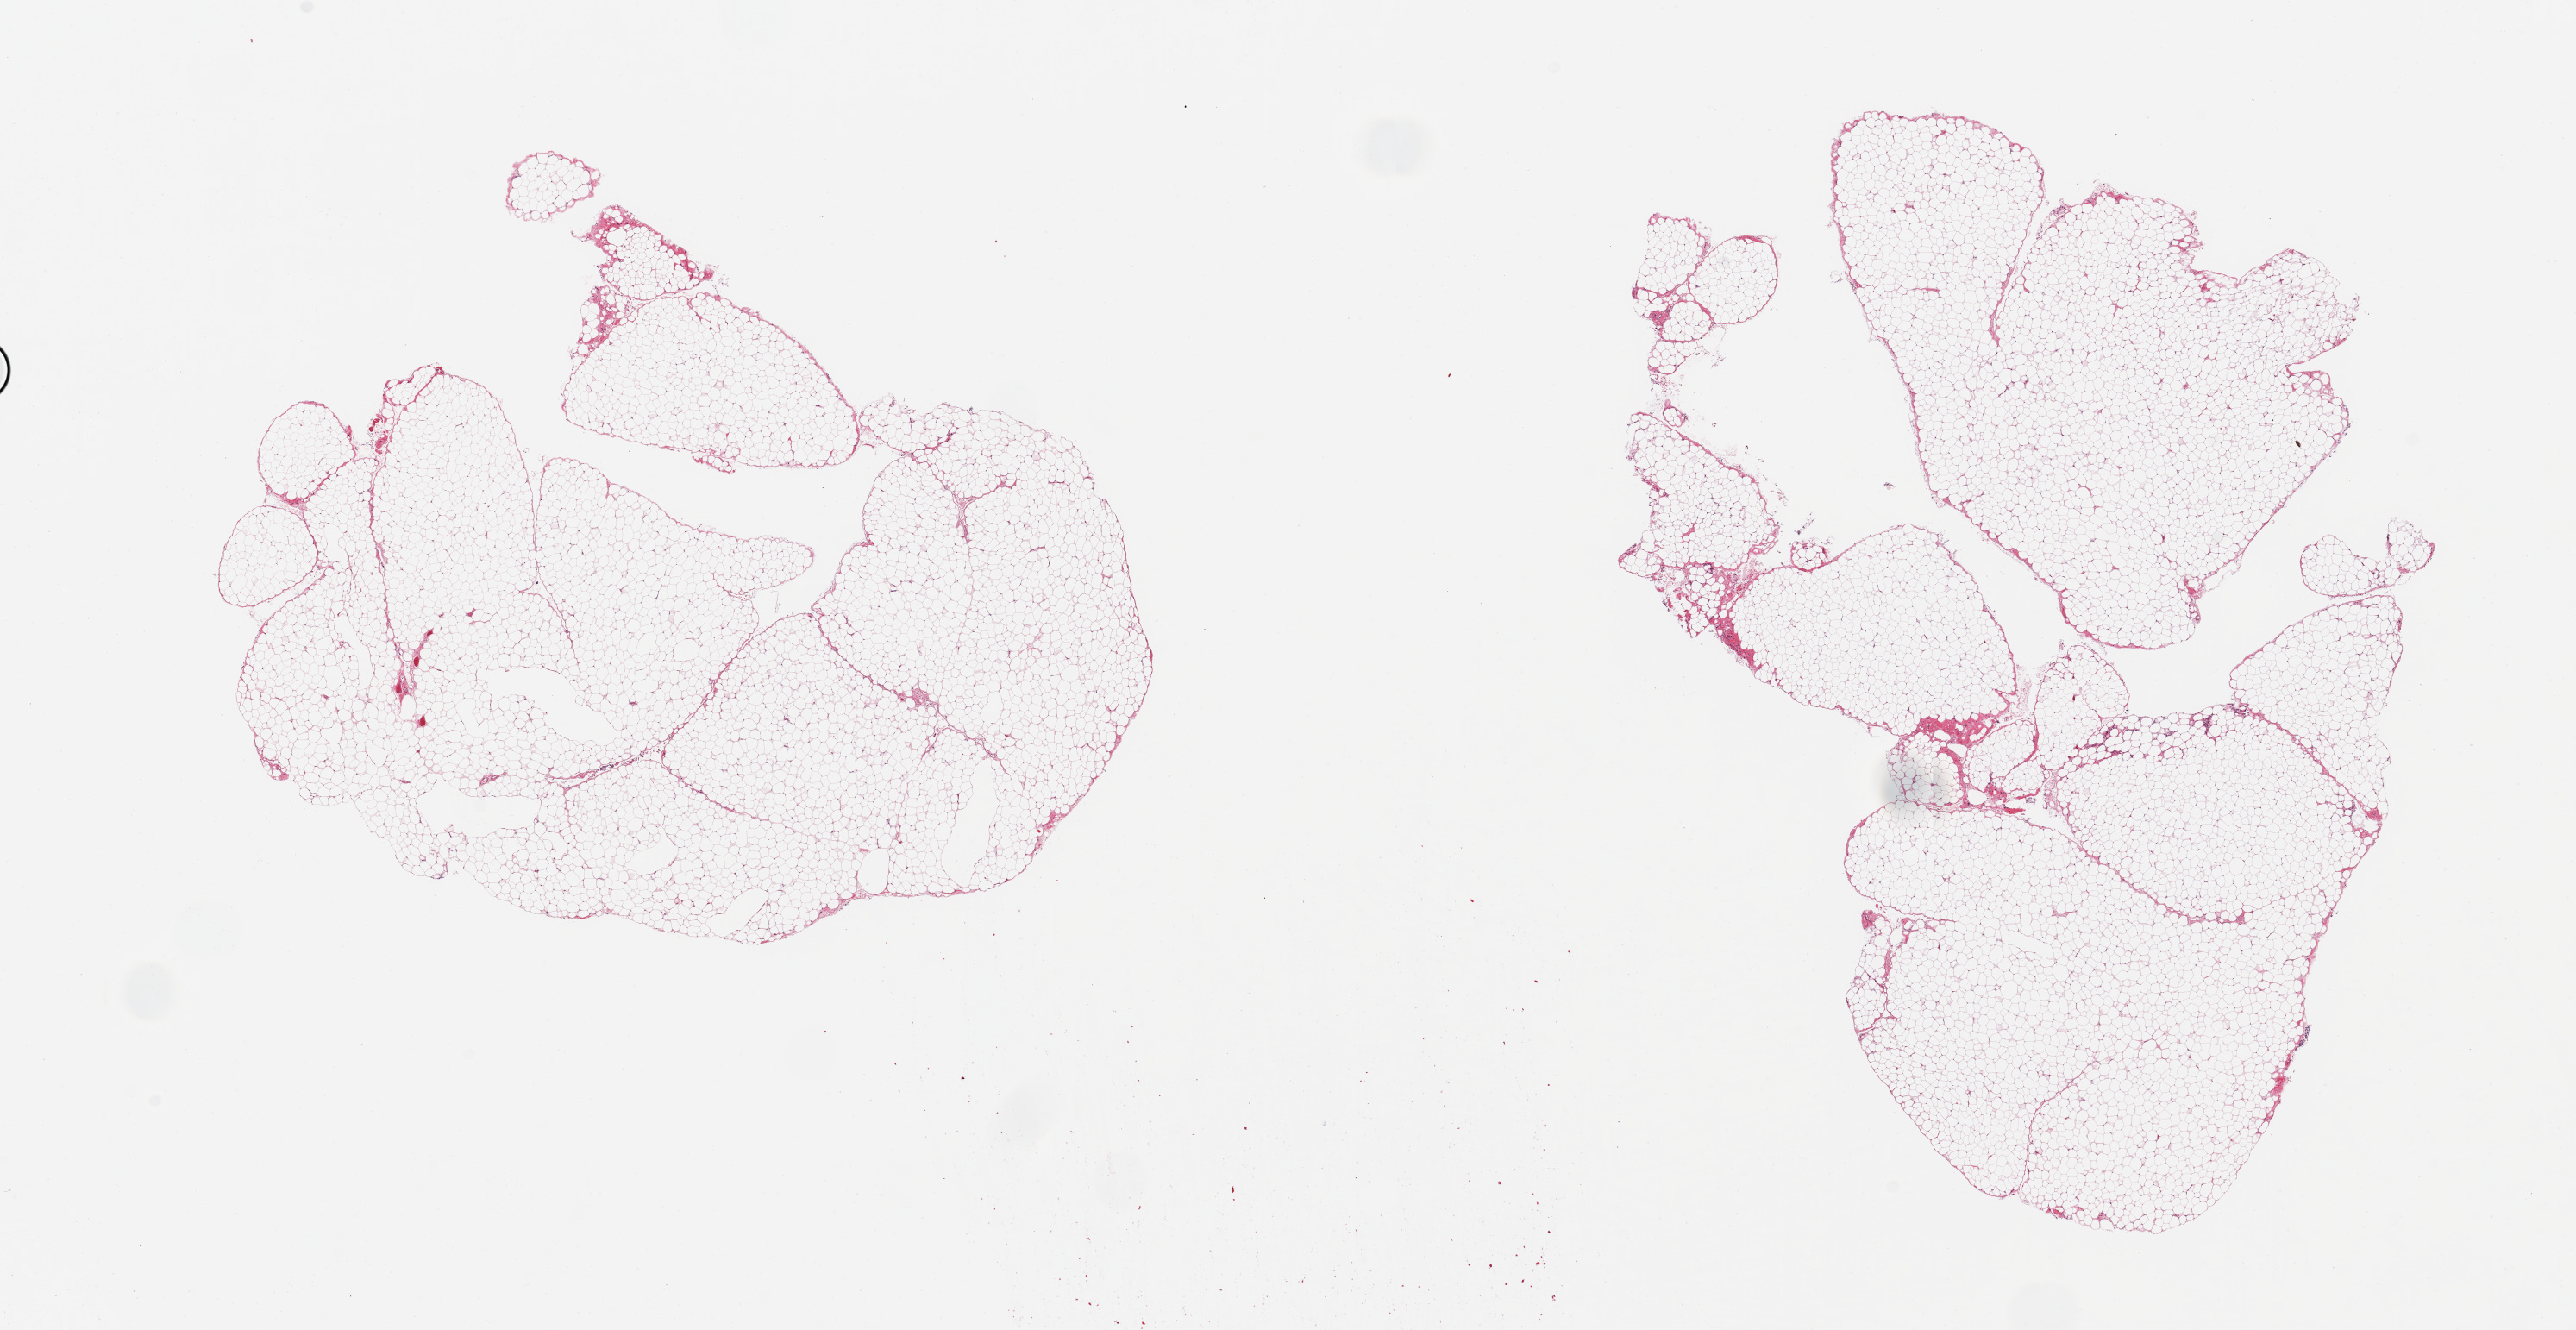
Whole-slide image, H&E stain, whole scanned area (about 23.6 x 12.2 mm, acquisition: 20x scan) shown as a low-resolution overview; PAXgene-fixed, paraffin-embedded tissue; target tissue: omentum; donor tissue sample. Donor: female.
* pathologist's review note for this sample: 2 pieces